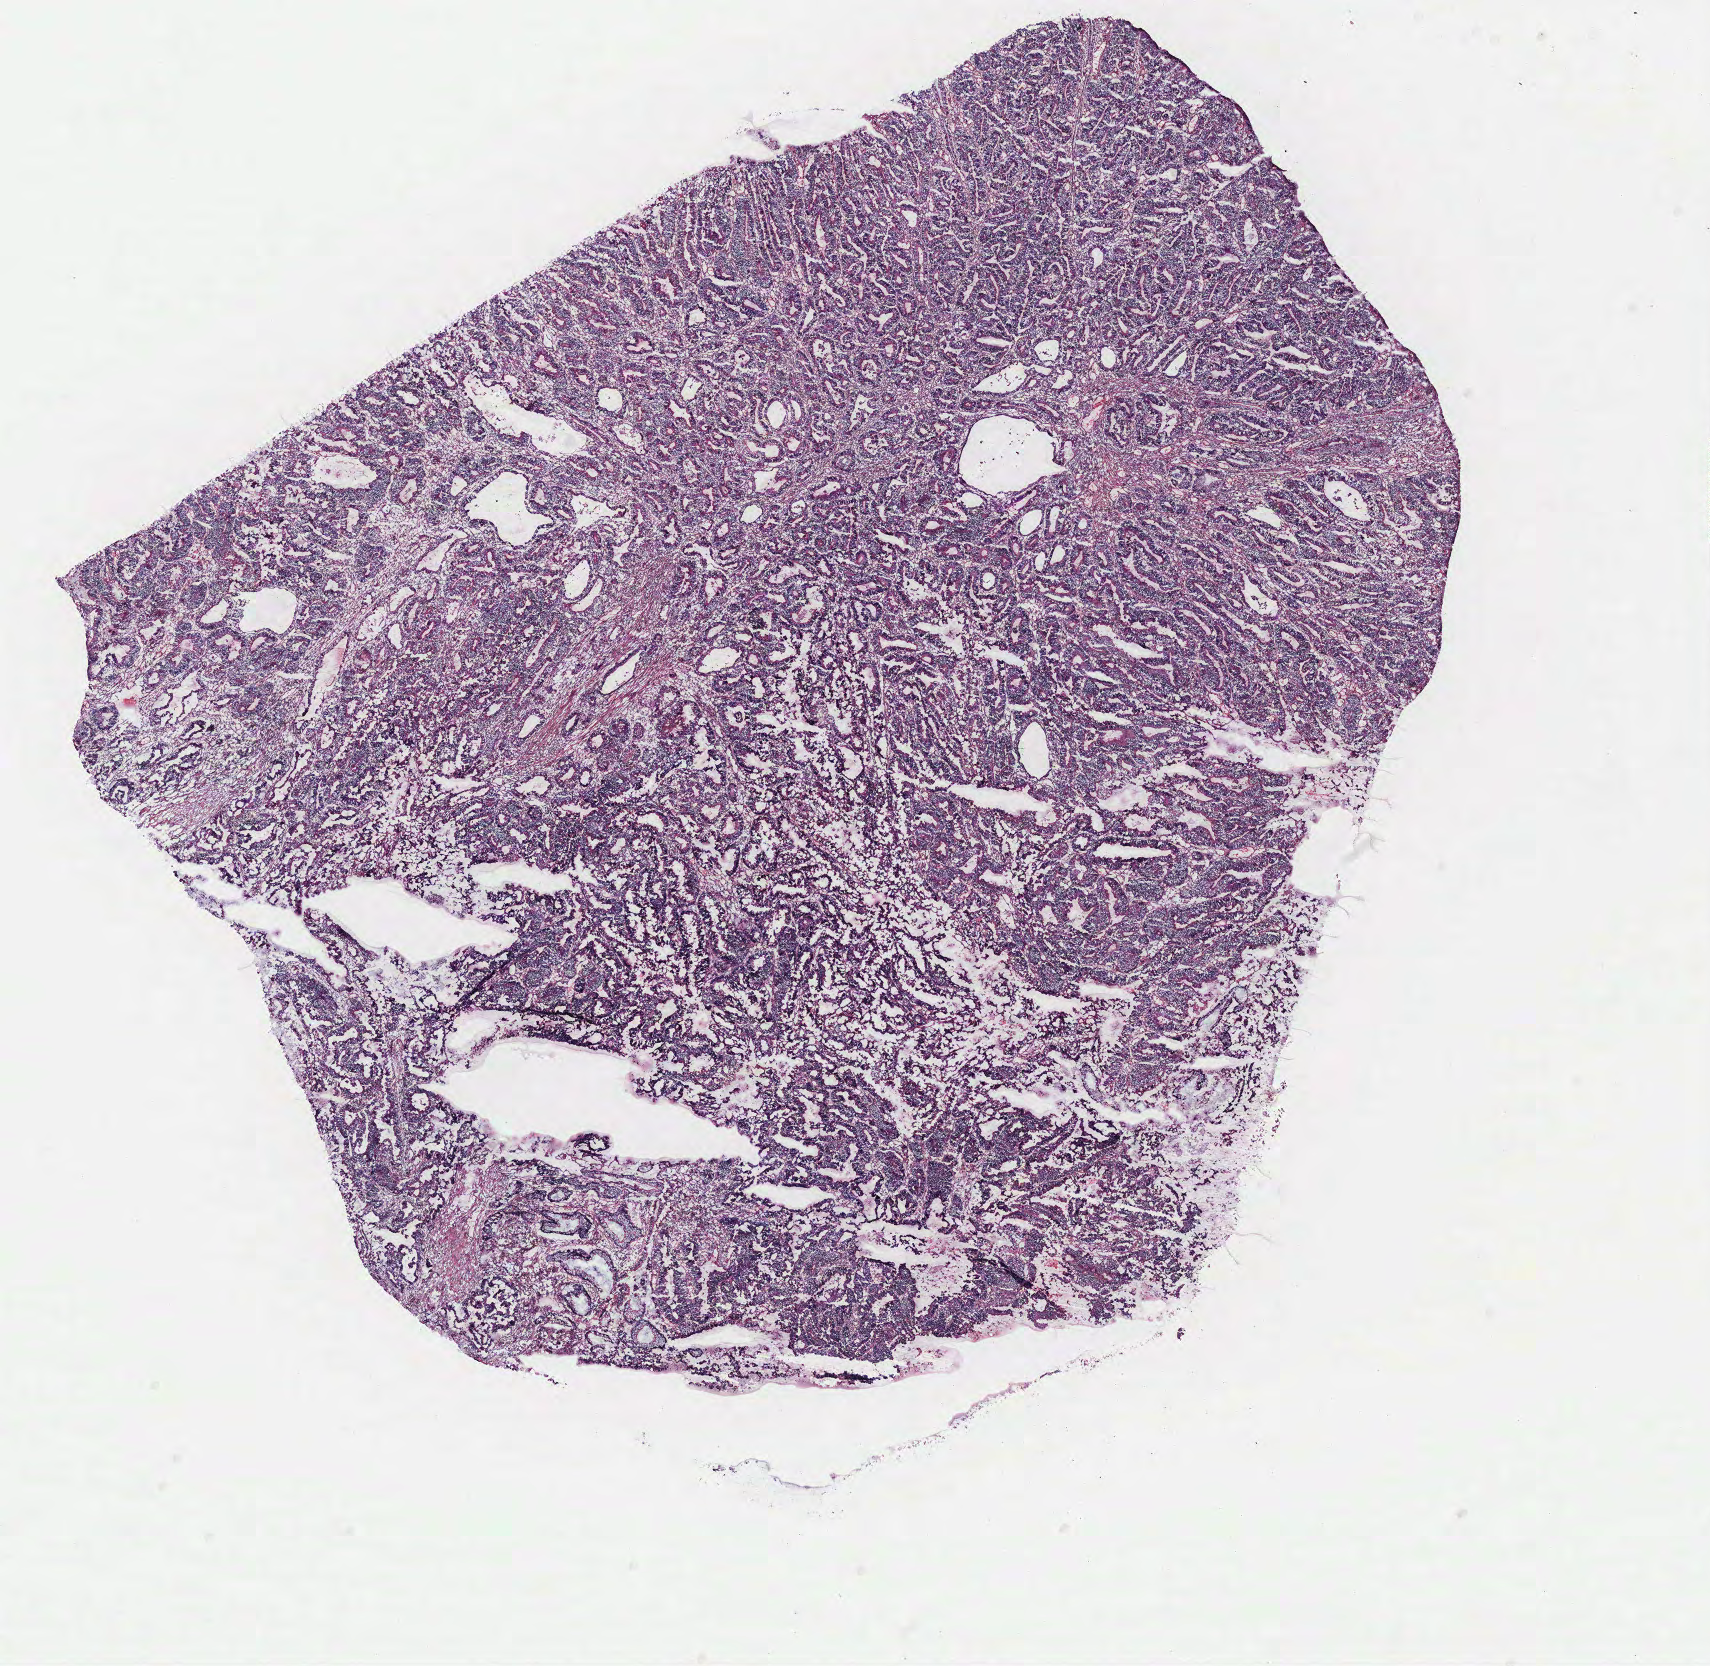
Hematoxylin and eosin (H&E) stained whole-slide image — a low-resolution overview of the entire scanned area, about 13.7 x 13.3 mm (from a 40x scan); colon, tumour tissue. 69-year-old female patient.
Diagnosis: Adenocarcinoma, NOS. AJCC pathologic stage: IIA. Primary tumour site (as recorded): colon.